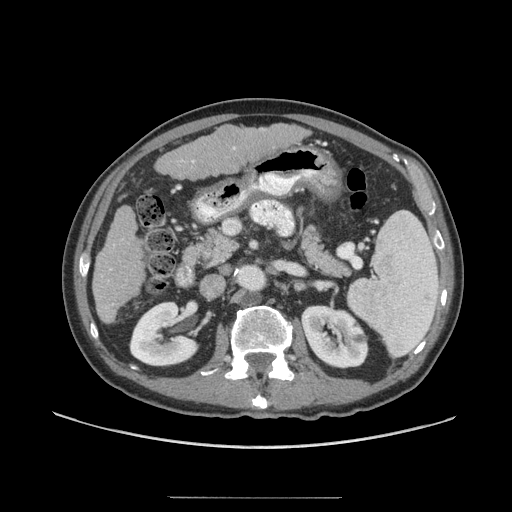
Contrast-enhanced abdominal CT (liver protocol), one axial slice. Position 22 of 71 along the scan axis. Soft-tissue window (W 400 / L 40 HU). 2.5 mm slice thickness. 512 × 512 image matrix, field of view 400 × 400 mm. Case-level facts recorded for this patient, not image findings: diagnosis: hepatocellular carcinoma (patient treated with transarterial chemoembolisation; whether this scan precedes or follows treatment is not stated here); TNM stage (as recorded): Stage-I; Child-Pugh class: A; tumour differentiation: well differentiated.
Annotated regions visible in this slice (semi-automatically segmented with operator editing):
- liver parenchyma outside the tumour (the mass and vessels are separate outlines, so this box may not span the whole liver): bounding box (x1, y1, x2, y2) in pixels: (92, 124, 306, 324)
- liver vessels: (110, 147, 236, 271)